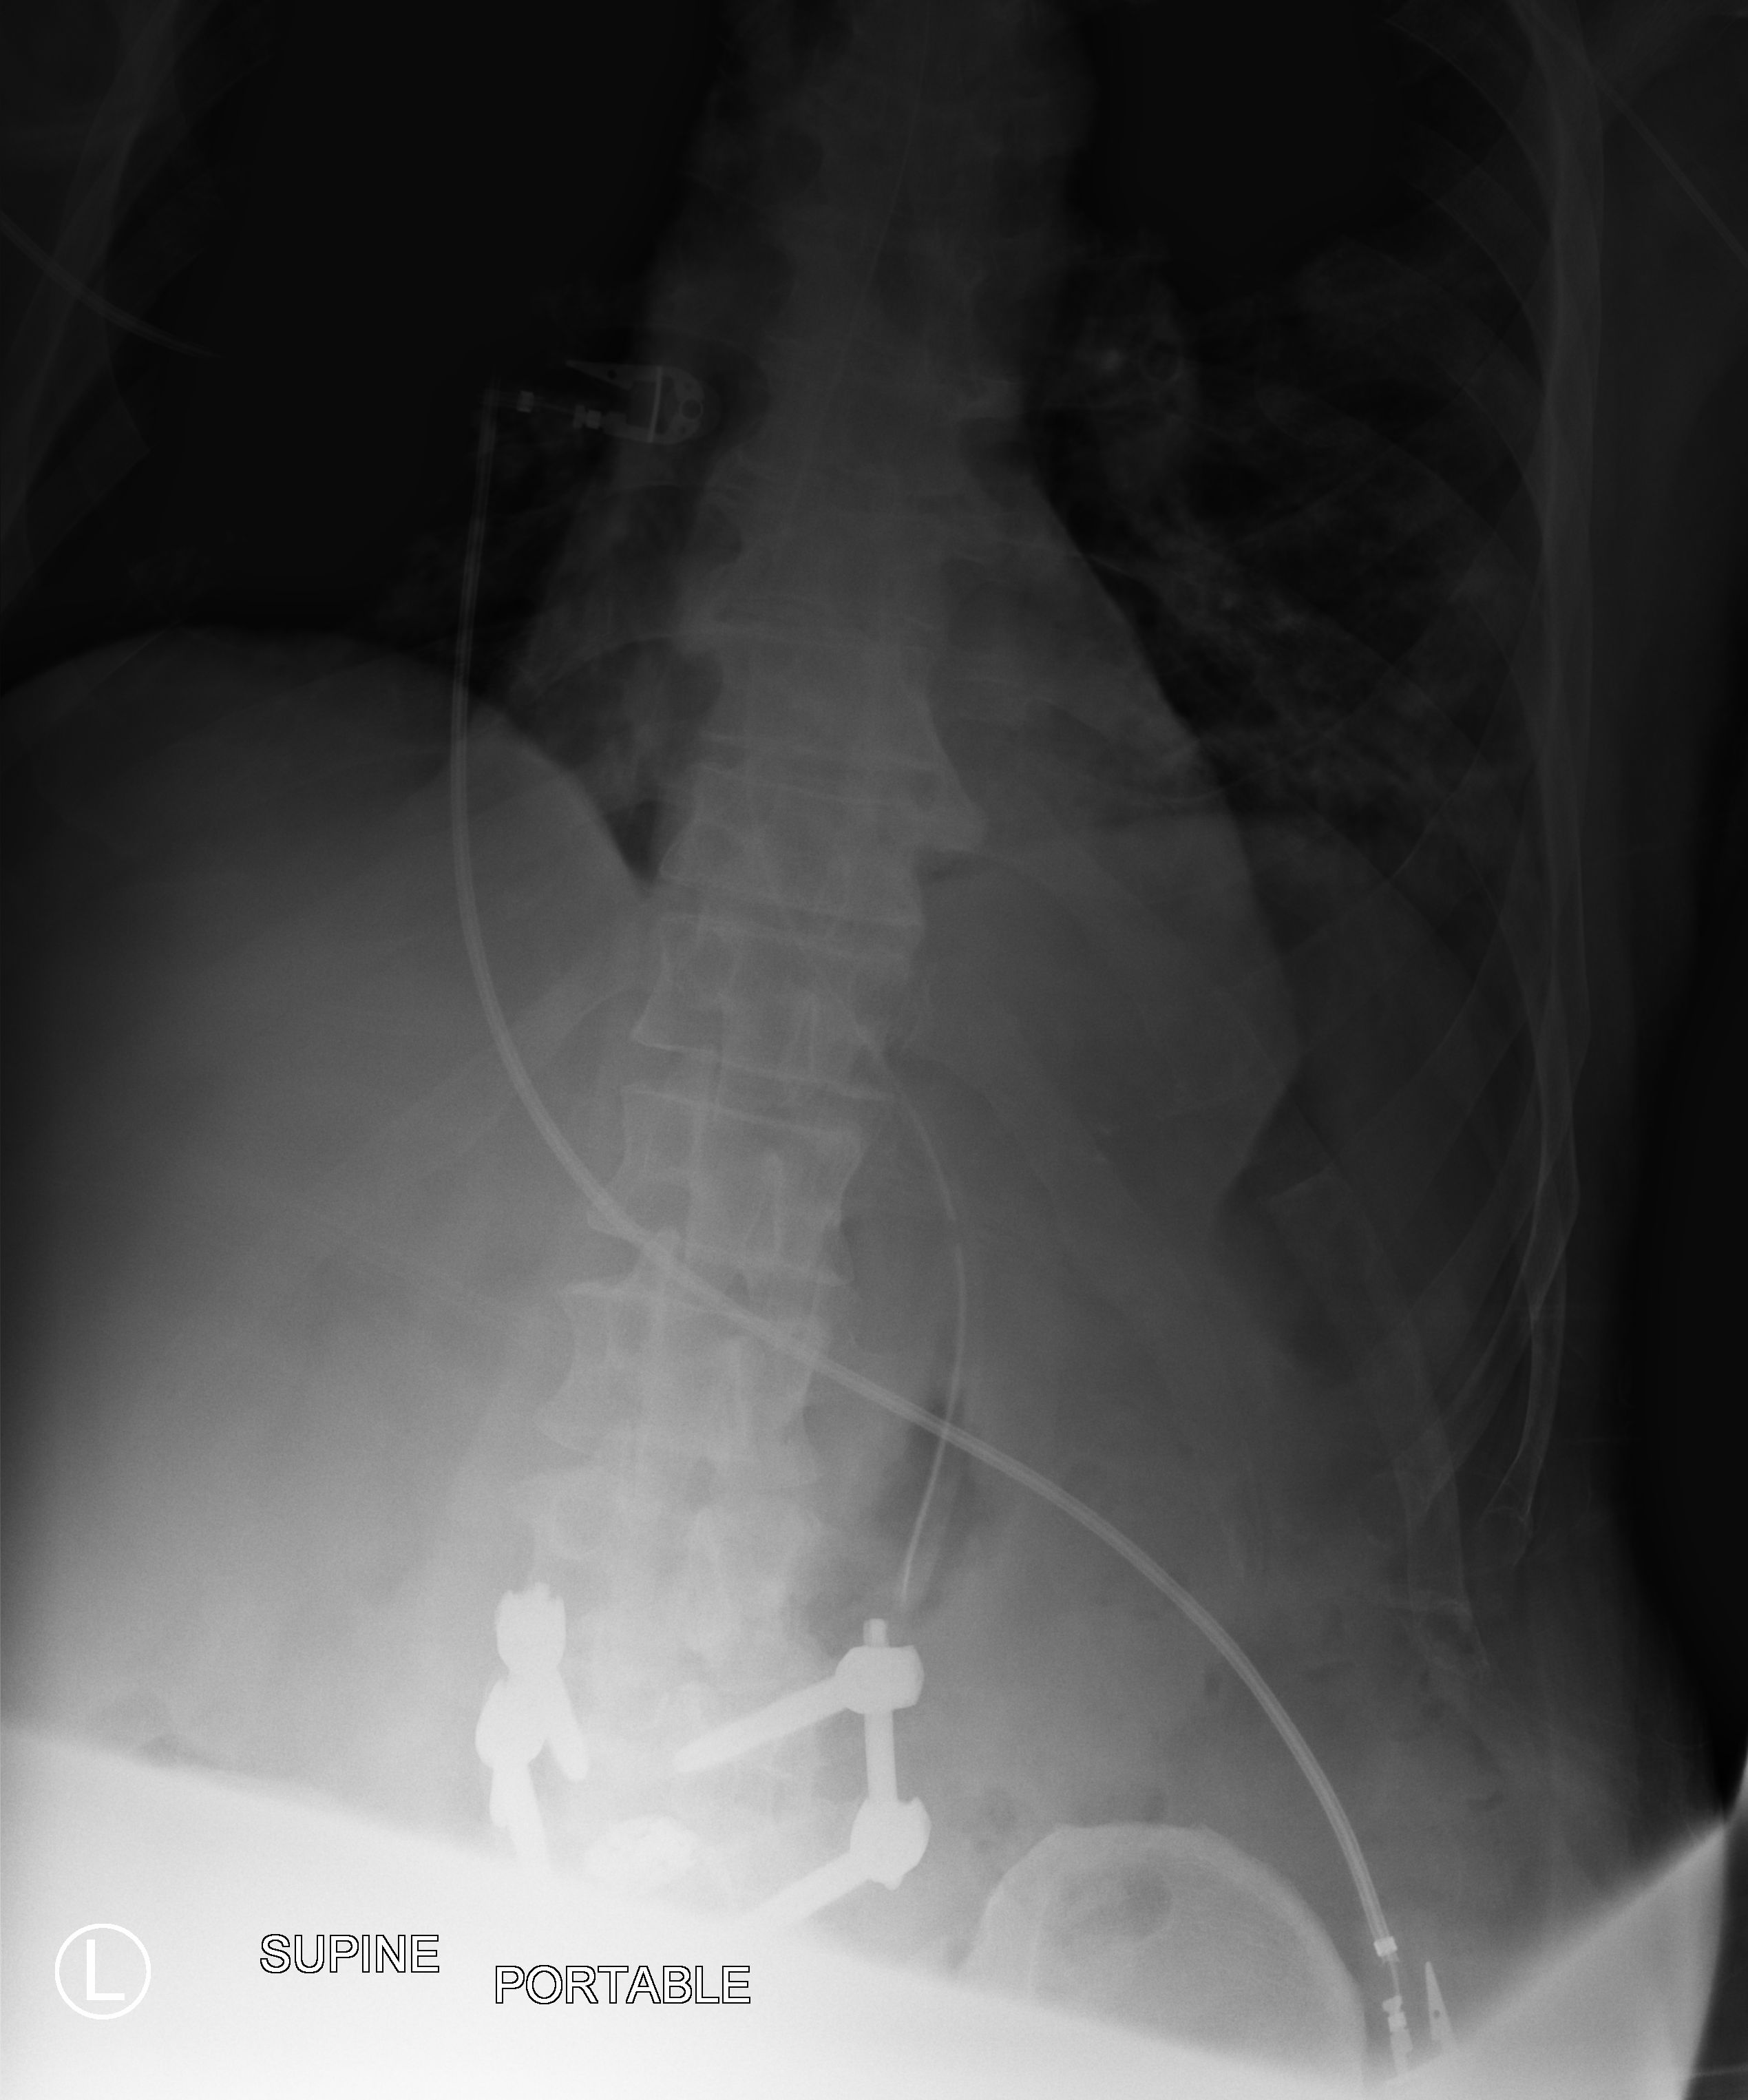
Abdomen radiograph. Male patient hospitalised with COVID-19, age 60–74 years.
From the hospital-stay record, not from the radiograph (when in the stay this image was taken is not recorded): mechanically ventilated during this hospital stay: yes; COPD (admission record): no; length of hospital stay: 35 days.